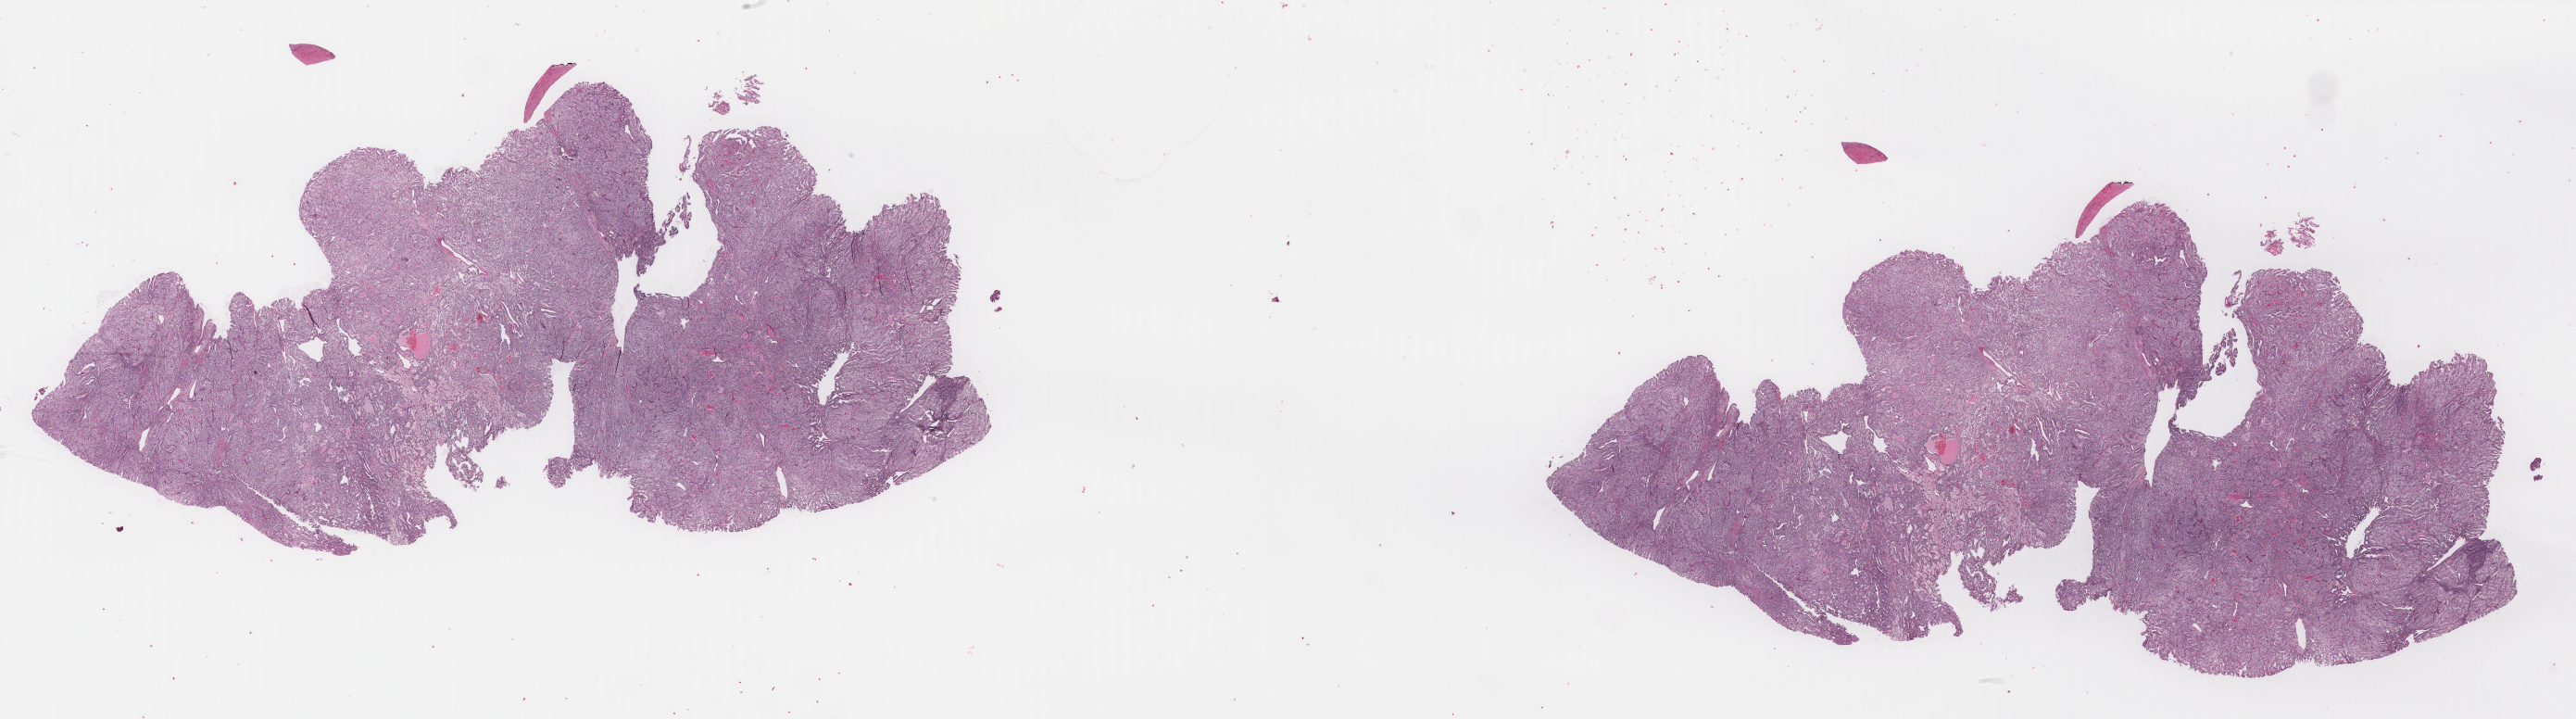
Digitized H&E tissue section (whole slide) — shown as a low-resolution overview of the whole scanned area (about 44.0 x 12.3 mm, from a 40x scan), formalin-fixed paraffin-embedded (FFPE) diagnostic section, kidney, primary tumour sample. Male patient; age at initial diagnosis 61 years. Histologic grade: G1 (well differentiated).
Diagnosis: Renal cell carcinoma, NOS. Laterality: right. AJCC pathologic stage: I.